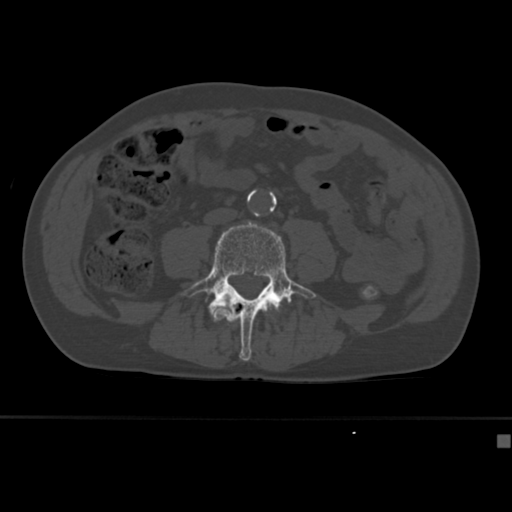
CT including the spine, one axial slice. Slice 108 of 430 in the series (ordered by position). Reconstruction kernel Br40s. 120 kVp. Bone window (W 1800 / L 400 HU). 512 × 512 image matrix, field of view 337 × 337 mm. Patient: male, 64 years. Case-level facts recorded for this patient, not image findings: primary cancer: uterus; vertebrae with lytic lesions (as recorded): T1, T4, T5, T7, L5.
Annotated regions visible in this slice (semi-automatically segmented with operator editing):
- L3 vertebra: bounding box (x1, y1, x2, y2) in pixels: (227, 299, 230, 310)
- L4 vertebra: (180, 220, 317, 361)